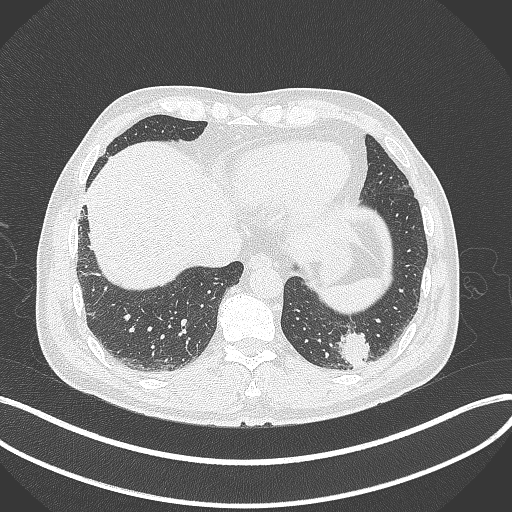
Chest CT, one axial slice. Position 61 of 300 along the scan axis. Reconstruction kernel B70f. 120 kVp. Lung window (W 1500 / L -600 HU). 1 mm slice thickness. 512 × 512 image matrix. Patient: male, 54 years. From the clinical record (not read from this slice): clinical TNM (as recorded): T1c N0 M1.
Structures marked on this image (bounding box drawn by a radiologist):
- lung tumour (recorded histology: adenocarcinoma): bounding box [x1, y1, x2, y2] px = [333, 328, 369, 366]